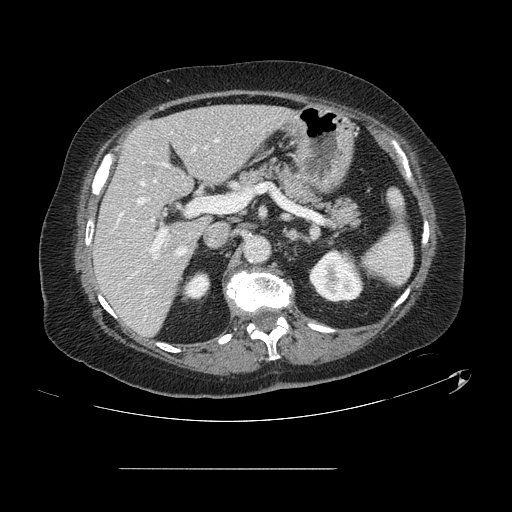
Contrast-enhanced abdominal CT, one axial slice; position 70 of 148 along the scan axis; 120 kVp; intravenous contrast given; soft-tissue window (W 400 / L 40 HU); 2.5 mm slice thickness; 512 × 512 image matrix, field of view 439 × 439 mm. Female patient, age 75 years. Case-level facts recorded for this patient, not image findings: diagnosis: colorectal cancer liver metastases, imaged before liver resection; multiple liver metastases: no; largest metastasis: 2.4 cm; chemotherapy before resection: no.
Structures marked on this image (outlined manually by an expert reader):
- hepatic veins: bounding box <120,139,218,255> (left, top, right, bottom; pixels)
- liver: <94,106,291,335>
- planned liver remnant (the part of the liver to remain after resection): <94,106,290,335>
- portal vein (with intrahepatic branches): <132,150,209,254>